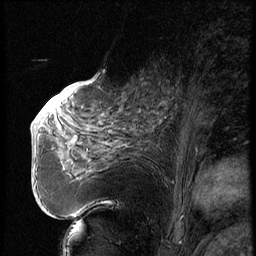
Breast MRI (dynamic contrast-enhanced), one sagittal slice; slice 34 of 74 in the series (ordered by position); dynamic contrast-enhanced series, image 2 of 3 at this slice position (ordered by acquisition); 1.5 T; TE 4.2 ms, TR 9 ms; 2.5 mm slice thickness; 256 × 256 image matrix. Female patient, age 56 years. From the clinical record (not read from this slice): setting: breast cancer imaged before/during neoadjuvant chemotherapy.
Annotated regions visible in this slice (semi-automatically segmented with operator editing):
- analysis volume of interest (the breast-tissue region the enhancement analysis was run in; not a lesion): box from (x=123, y=71) to (x=195, y=131) px
- tumour enhancement mask (voxels above the 140 % enhancement threshold inside the analysis volume of interest): (x=160, y=116)–(x=166, y=124)